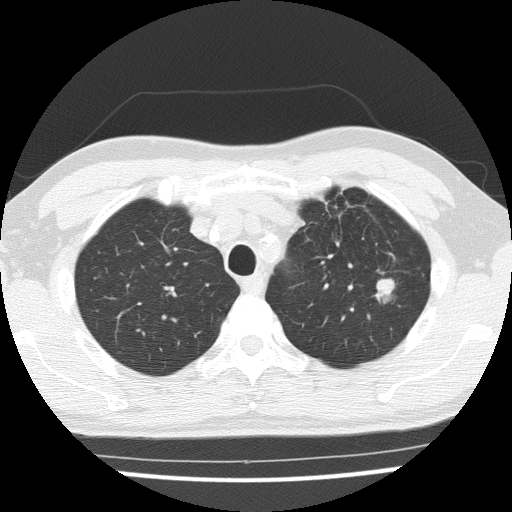
Low-dose screening chest CT, axial slice. Third annual screen. Lung window (W 1500 / L -600 HU). 2 mm slice thickness. Slice 37 of 154 in the series. 512 × 512 image matrix, field of view 330 × 330 mm. Male, age 65 years at enrolment. Current smoker at enrolment.
Lesion marked by an expert reader, box from (x=355, y=270) to (x=408, y=315) px. The exam's reader record, not a measurement of the box and not confirmed to be the same lesion: non-calcified nodule or mass ≥4 mm, left upper lobe, 16 × 15 mm, poorly defined margins, soft tissue attenuation, pre-existing on the prior screen: yes; interval growth: yes. Participant outcome: lung cancer diagnosed 42 days after this screen — squamous cell carcinoma, NOS, left upper lobe, moderately differentiated (G2), stage IA (AJCC 6th edition), 25 mm at pathology.